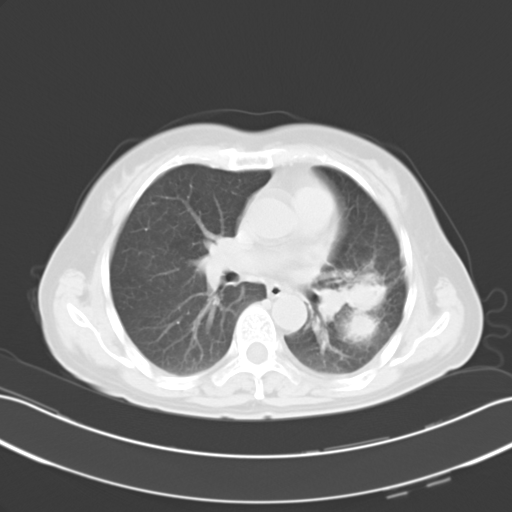
Chest CT, one axial slice; slice 14 of 25 in the series (ordered by position); reconstruction kernel B40f; 120 kVp; lung window (W 1500 / L -600 HU); 10 mm slice thickness; 512 × 512 image matrix, field of view 353 × 353 mm. Patient: female, 54 years. From the clinical record (not read from this slice): clinical TNM (as recorded): T3 N1 M0.
Annotated regions visible in this slice (bounding box drawn by a radiologist):
- lung tumour (recorded histology: adenocarcinoma): bounding box (x1, y1, x2, y2) in pixels: (322, 270, 389, 340)